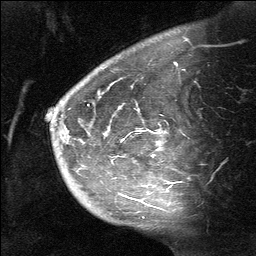
Breast MRI (dynamic contrast-enhanced), one sagittal slice; dynamic contrast-enhanced study with each time point stored as its own series, time point 2 of 3 at this slice position (early post-contrast, ordered by acquisition time); 1.5 T; TE 4.8 ms, TR 27 ms; 2 mm slice thickness; 256 × 256 image matrix, field of view 180 × 180 mm. Female patient, age 39 years. From the clinical record (not read from this slice): setting: breast cancer imaged before/during neoadjuvant chemotherapy; receptor status: HER2-positive.
Outlined on this slice (semi-automatically segmented with operator editing):
- analysis volume of interest (the breast-tissue region the enhancement analysis was run in; not a lesion): box from (x=58, y=40) to (x=196, y=217) px
- tumour enhancement mask (voxels above the 90 % enhancement threshold inside the analysis volume of interest): (x=122, y=109)–(x=149, y=206)